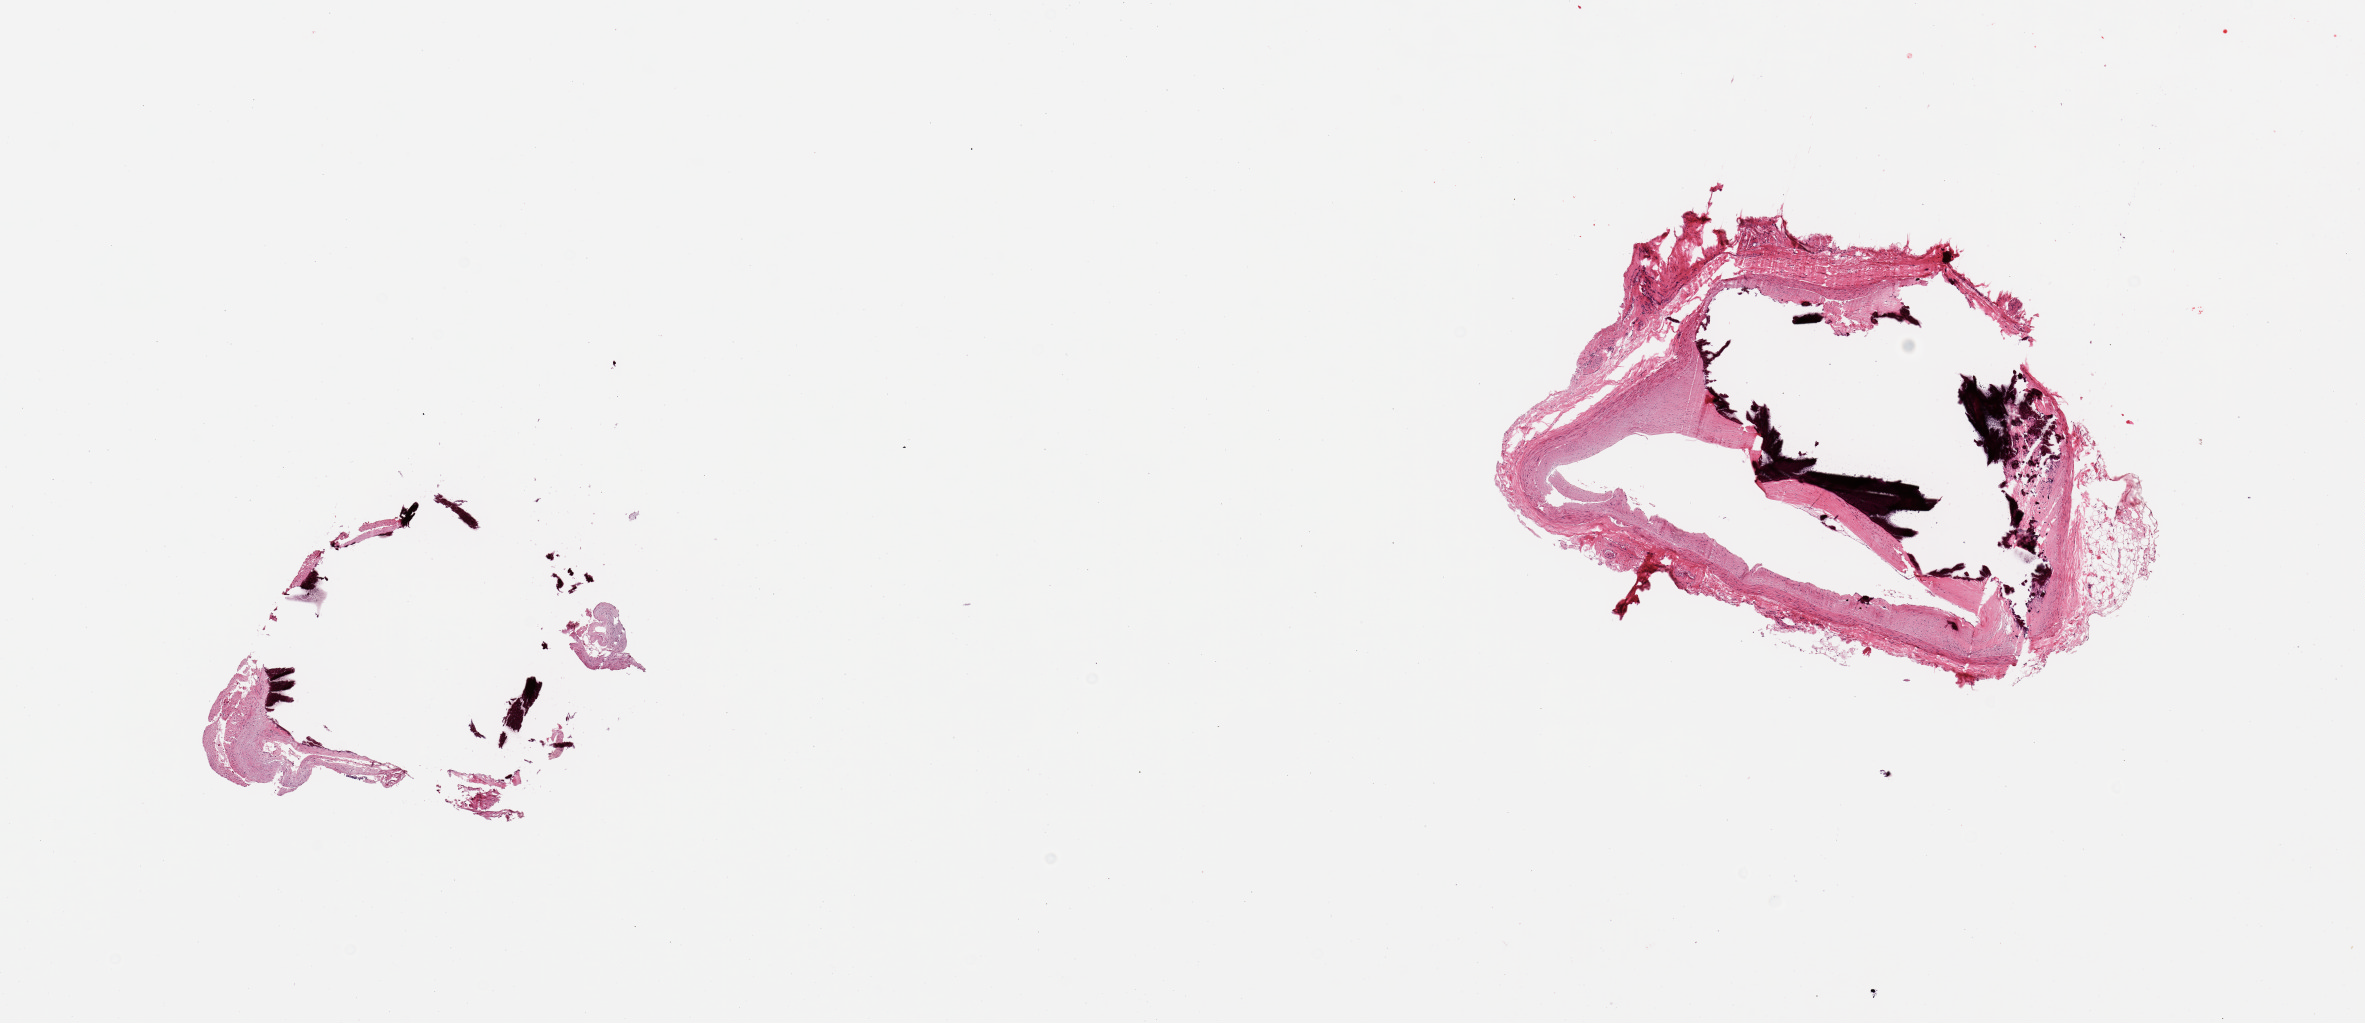
H&E whole-slide image, brightfield, shown as a low-resolution overview of the whole scanned area (about 18.7 x 8.1 mm, slide scanned at 20x). PAXgene-fixed paraffin-embedded (PFPE) section. Target tissue: coronary artery. Donor tissue sample. Male donor.
- reviewer comment on this tissue sample: 2 fragmented pieces; excessively calcified and fragmented; 10% normal target remains